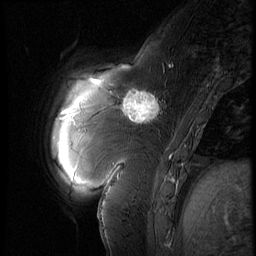
Breast MRI (dynamic contrast-enhanced), one sagittal slice. Position 16 of 60 along the scan axis. 3 images stored at this slice position (order not interpretable as contrast timing). 1.5 T. TE 4.2 ms, TR 9 ms. 2.5 mm slice thickness. 256 × 256 image matrix, field of view 180 × 180 mm. Patient: female, 57 years. Case-level facts recorded for this patient, not image findings: setting: breast cancer imaged before/during neoadjuvant chemotherapy; receptor status: triple-negative.
Outlined on this slice (semi-automatic segmentation, software-assisted and operator-edited):
- analysis volume of interest (the breast-tissue region the enhancement analysis was run in; not a lesion): bounding box (x1, y1, x2, y2) in pixels: (114, 83, 170, 131)
- tumour enhancement mask (voxels above the 140 % enhancement threshold inside the analysis volume of interest): (122, 91, 159, 125)